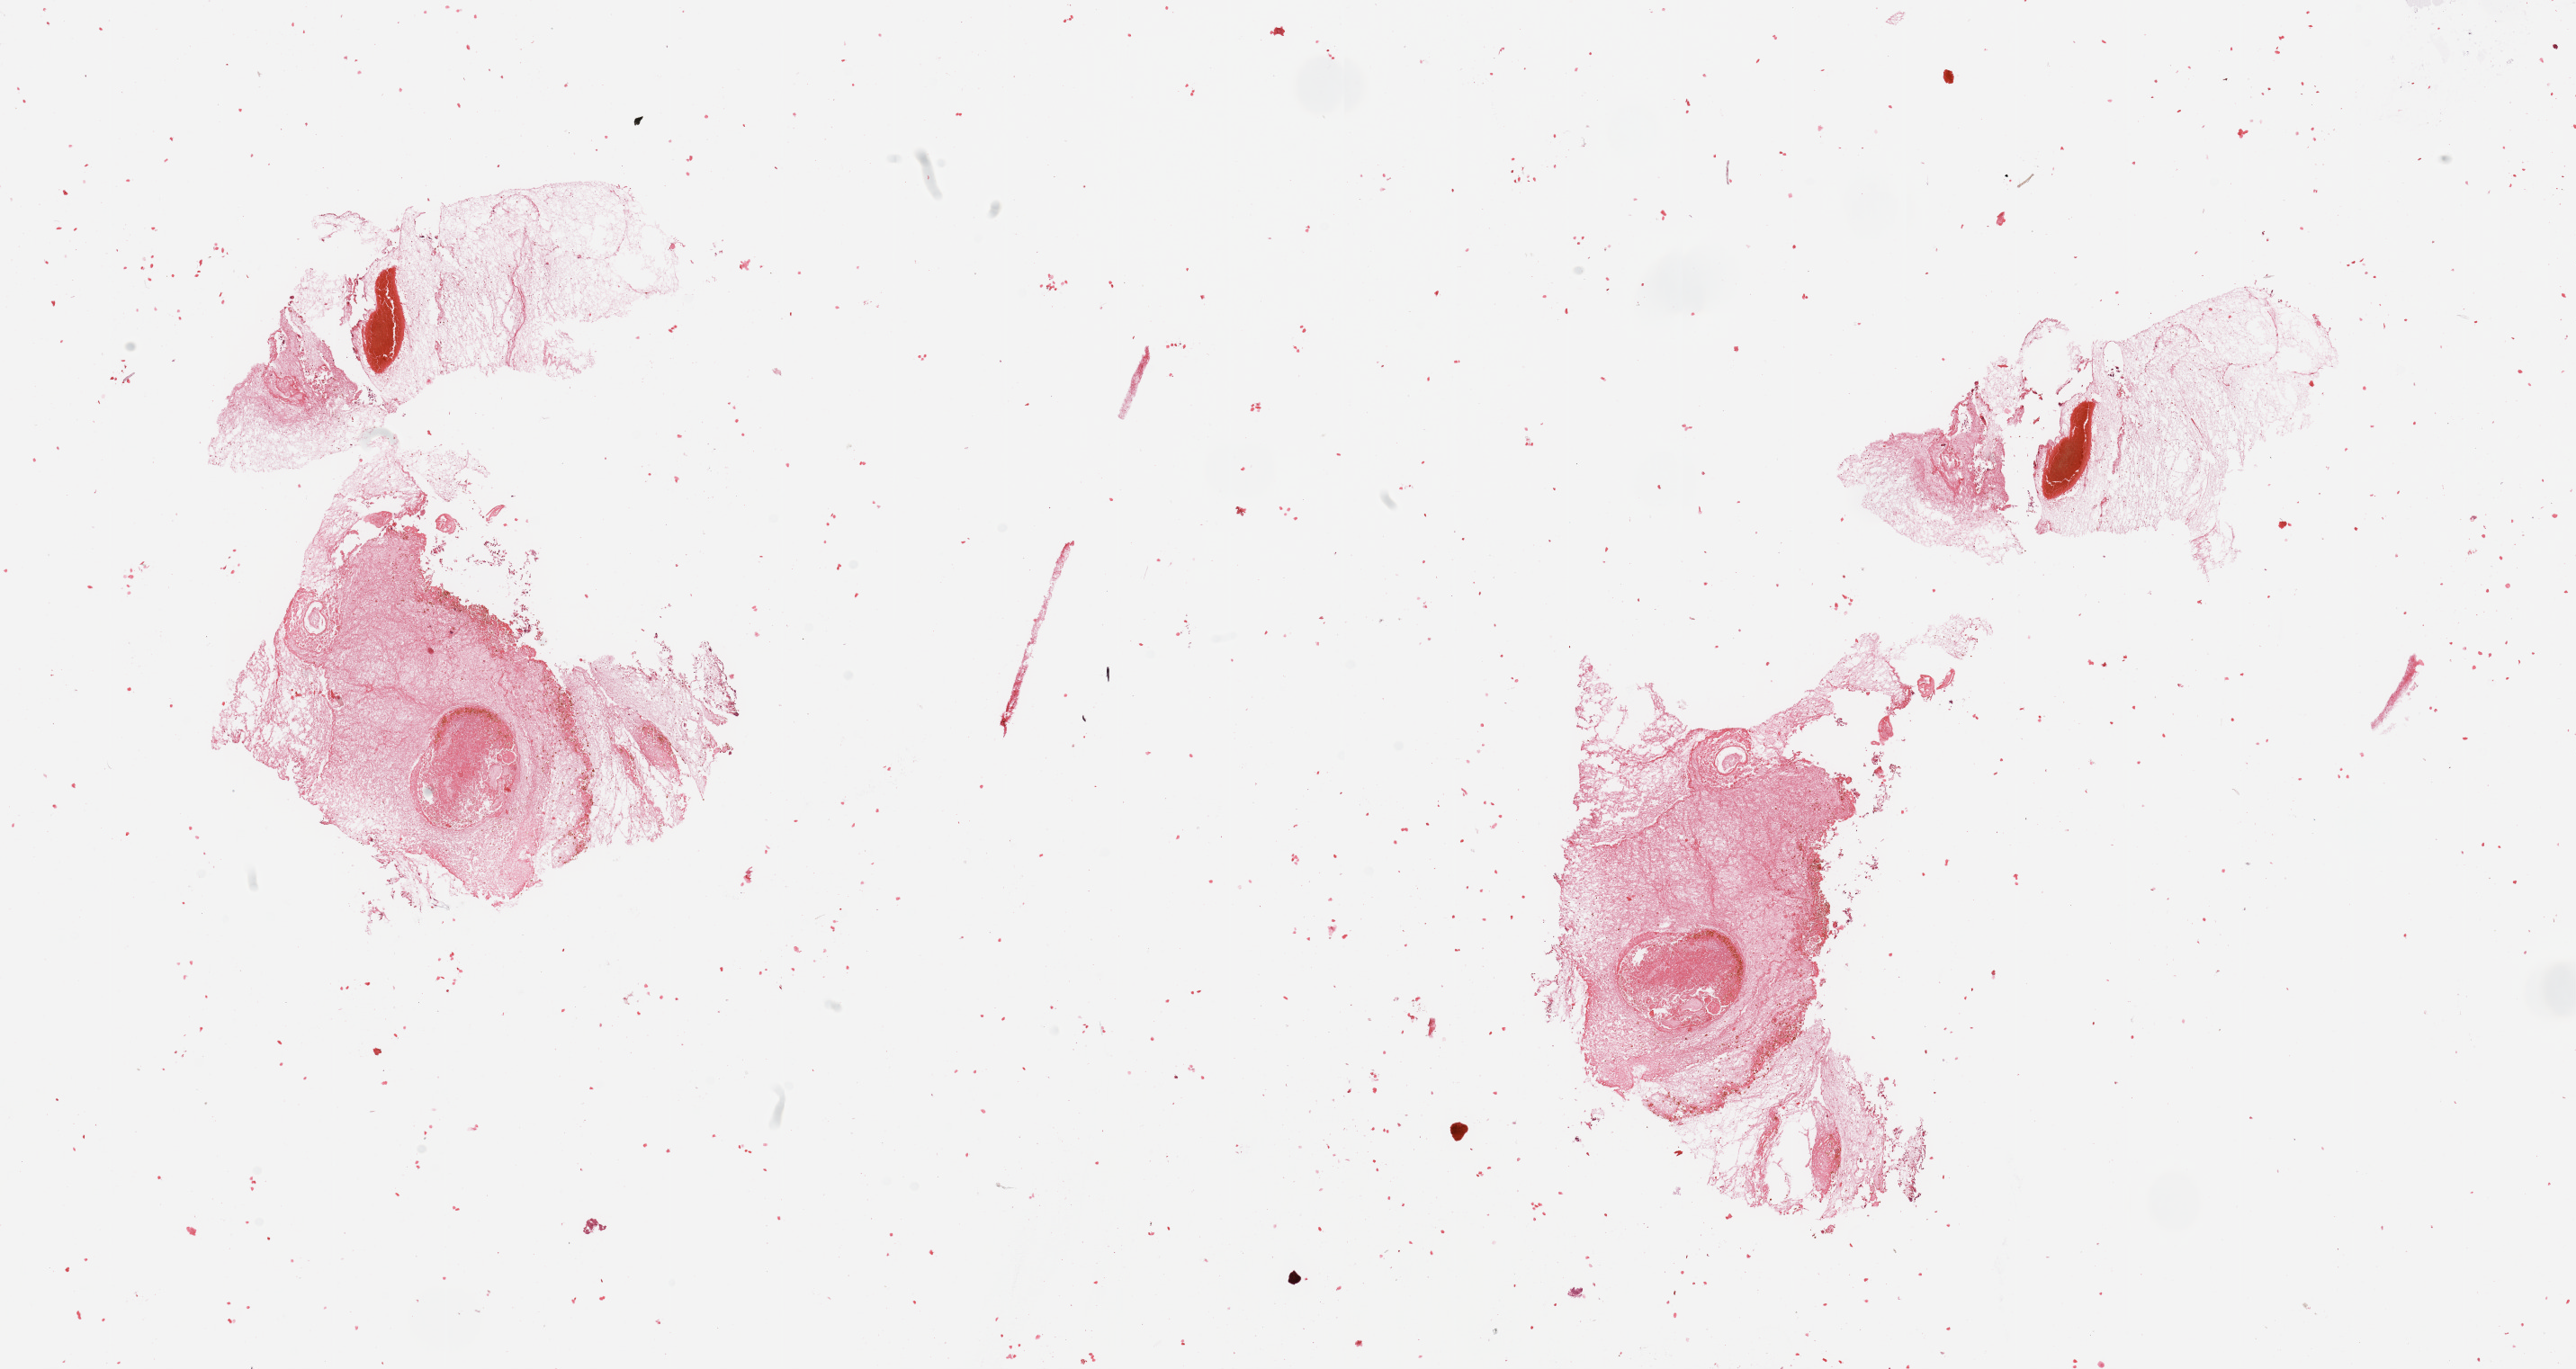
Digitized H&E-stained tissue section (whole slide) — shown as a low-resolution overview of the whole scanned area (about 22.6 x 12.0 mm, slide scanned at 20x); brain, tumour tissue. Patient: male, age 39 years.
Diagnosis: Glioblastoma.